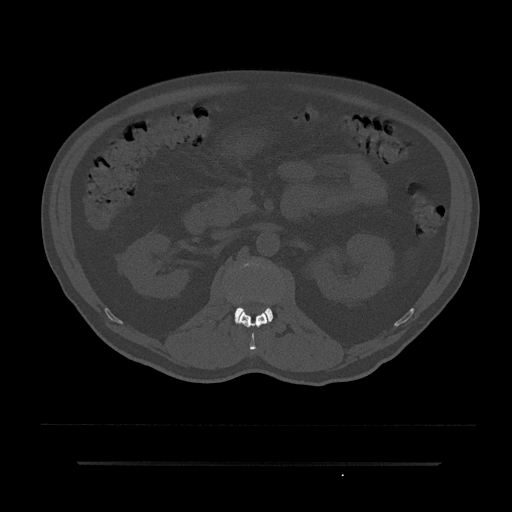
CT including the spine, one axial slice; position 111 of 797 along the scan axis; reconstruction kernel Br40s/3; 120 kVp; bone window (W 1800 / L 400 HU); 0.5 mm slice thickness; 512 × 512 image matrix. Patient: male, 59 years. From the clinical record (not read from this slice): primary cancer: bile ducts.
Annotated regions visible in this slice (semi-automatically segmented with operator editing):
- L1 vertebra: box from (x=238, y=312) to (x=267, y=351) px
- L2 vertebra: (x=235, y=307)–(x=273, y=323)